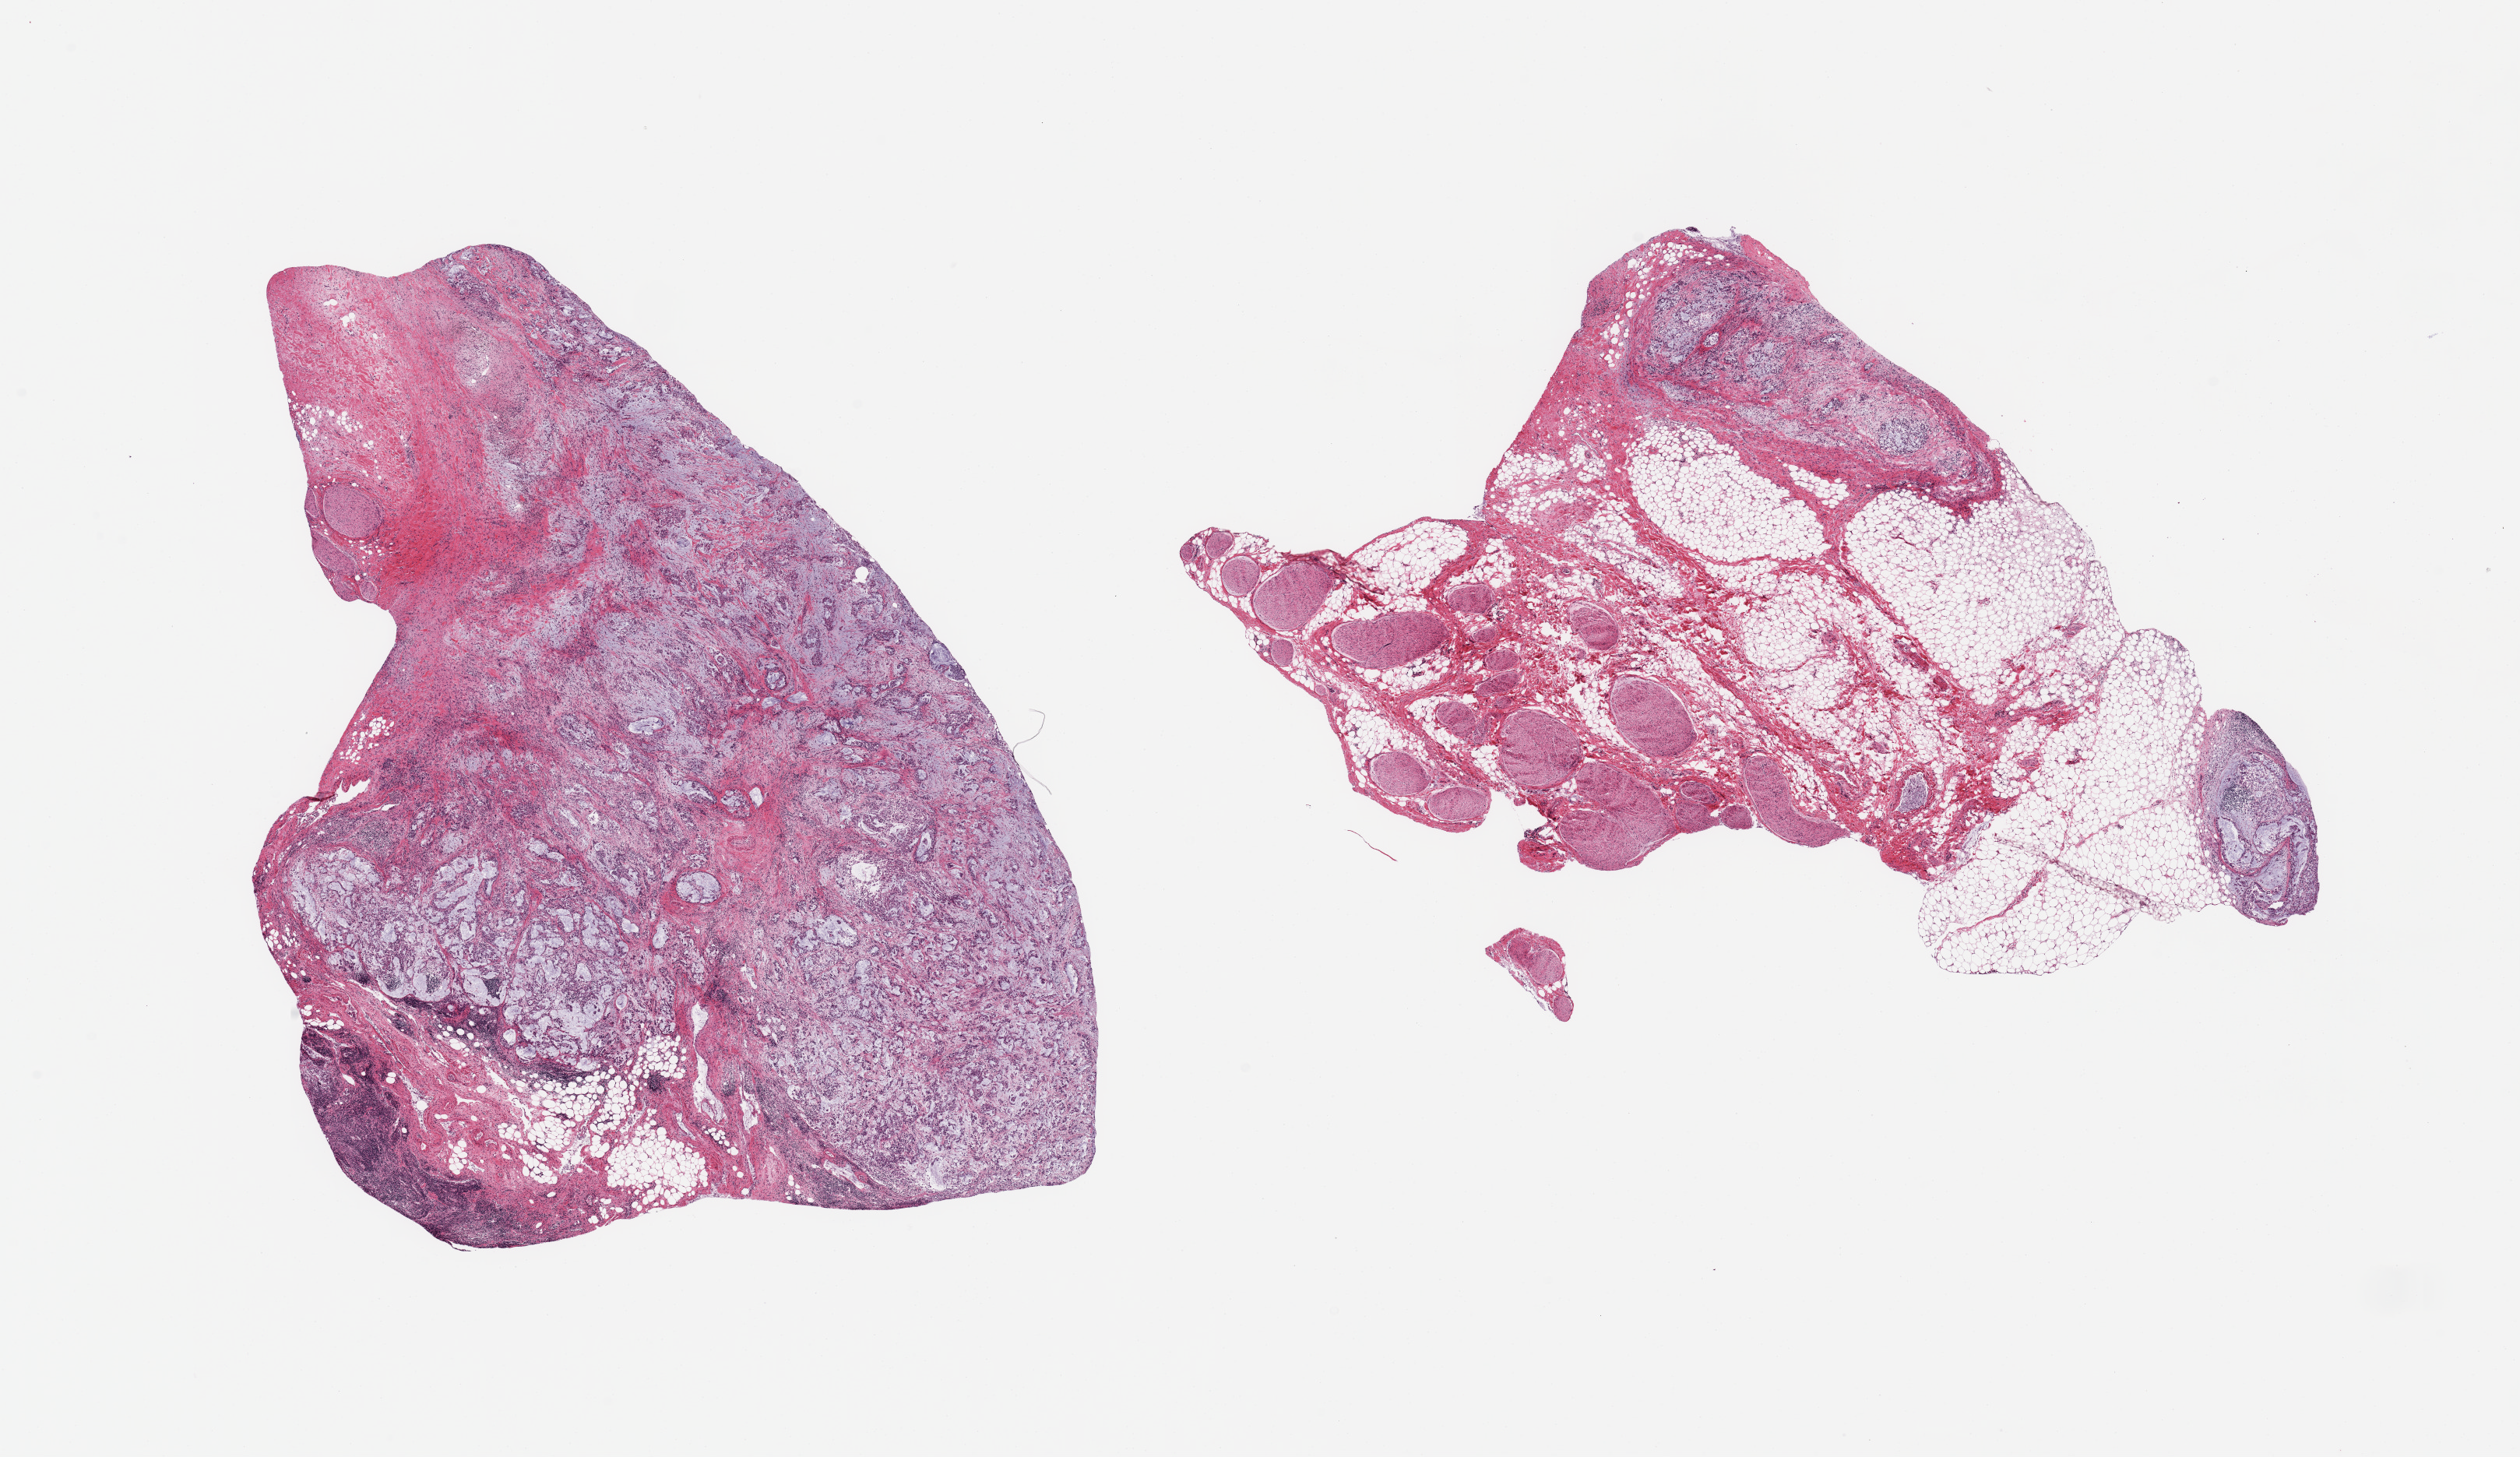
Whole-slide image, H&E stain — low-resolution overview of the scanned area, about 25.6 x 14.8 mm (slide scanned at 20x); PAXgene-fixed, paraffin-embedded tissue; target tissue: pancreas; tissue donor sample. Donor sex: male.
Reviewer comment on this tissue sample: 2 pieces, advanced saponification, histologic features completely degraded, ~50% fat.